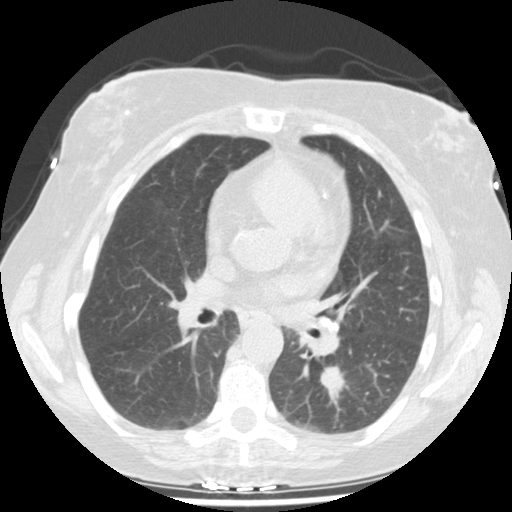
Axial slice from a low-dose chest CT screening exam; second screening round (one year after baseline); lung window (W 1500 / L -600 HU); 2.5 mm slice thickness; standard (soft-tissue) reconstruction kernel (STANDARD); 120 kVp. Female, age 61 years at enrolment. Current smoker at enrolment.
Lesion marked by an expert reader, bounding box [x1, y1, x2, y2] px = [312, 354, 363, 406]. The screening reader recorded 2 non-calcified nodules or masses ≥4 mm on this exam (left lower lobe, right upper lobe); which of them this box marks is not recorded. Official screen result: positive, change unspecified: nodule(s) >= 4 mm or enlarging nodule(s), mass(es), or other non-specific abnormalities suspicious for lung cancer. Lung cancer was diagnosed 69 days after this screen: squamous cell carcinoma, NOS, left lower lobe, moderately differentiated (G2), stage IA (AJCC 6th edition), 12 mm at pathology.